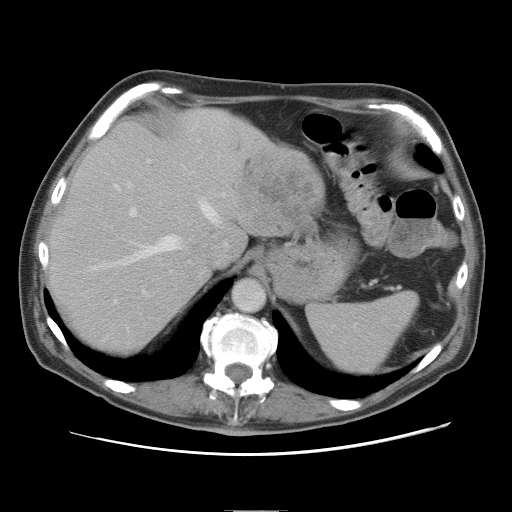
Contrast-enhanced abdominal CT, one axial slice. Slice 61 of 89 in the series (ordered by position). 120 kVp. Intravenous contrast given. Soft-tissue window (W 400 / L 40 HU). 5 mm slice thickness. 512 × 512 image matrix, field of view 375 × 375 mm. Male patient, age 69 years. Case-level facts recorded for this patient, not image findings: diagnosis: colorectal cancer liver metastases, imaged before liver resection; multiple liver metastases: no; largest metastasis: 8.5 cm.
Annotated regions visible in this slice (expert manual segmentation):
- hepatic veins: bounding box [x1, y1, x2, y2] px = [94, 184, 221, 269]
- liver: [51, 109, 323, 351]
- planned liver remnant (the part of the liver to remain after resection): [51, 109, 246, 351]
- portal vein (with intrahepatic branches): [129, 141, 201, 217]
- liver metastasis: [234, 153, 318, 226]